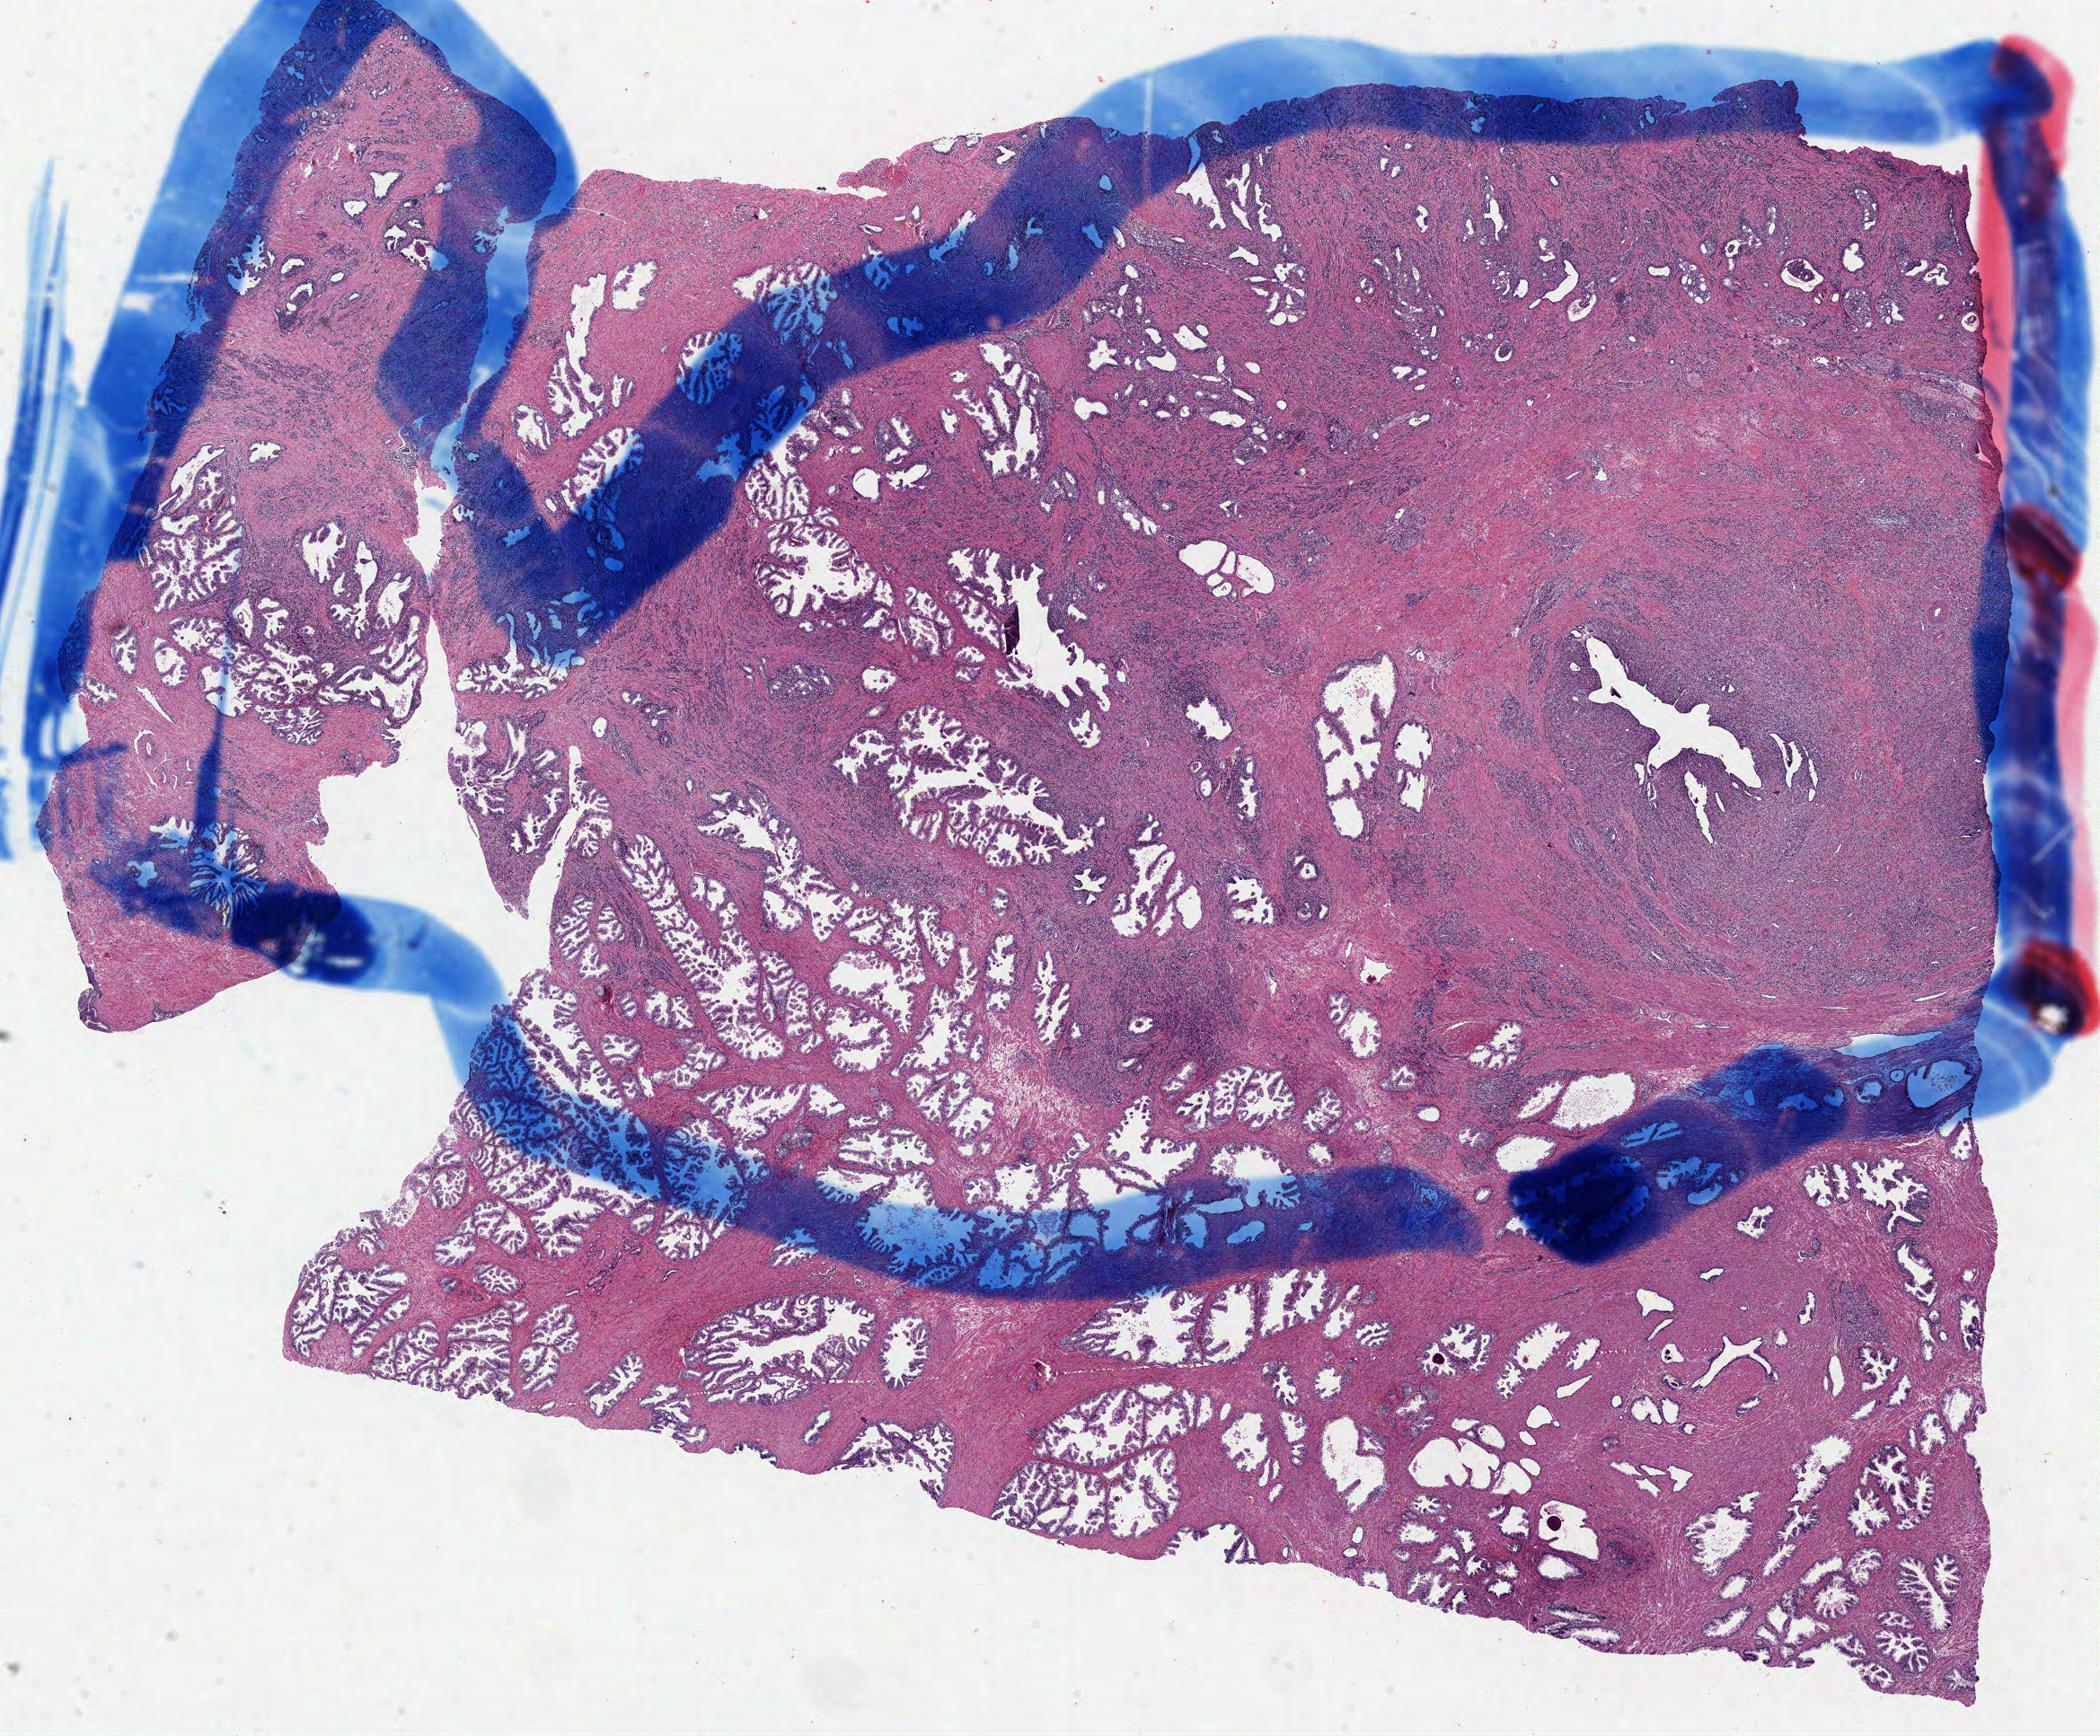
Whole-slide histology image, Hematoxylin and eosin (H&E) stained, low-resolution overview of the scanned area, about 18.9 x 15.6 mm (slide scanned at 40x). Formalin-fixed paraffin-embedded (FFPE) diagnostic section. Primary tumour sample from the prostate. Male patient; age at initial diagnosis 67 years. Gleason score: 8 (5+3).
Lymph nodes positive (case pathology): 1 of 7 examined. Pathologic diagnosis: Acinar cell carcinoma (prostate gland).